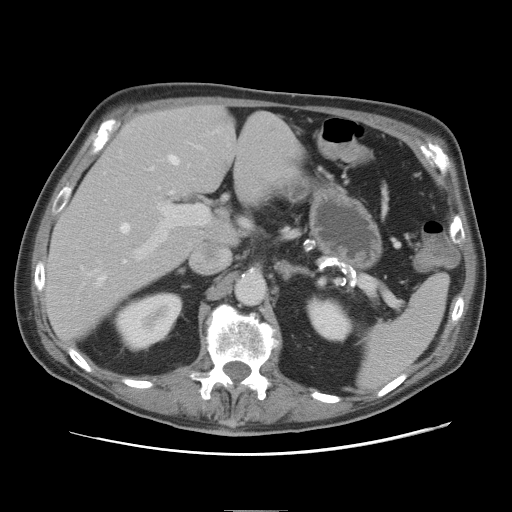
Contrast-enhanced abdominal CT, one axial slice; intravenous contrast given; soft-tissue window (W 400 / L 40 HU); 5 mm slice thickness; 512 × 512 image matrix, field of view 375 × 375 mm. Male patient, age 69 years. From the clinical record (not read from this slice): diagnosis: colorectal cancer liver metastases, imaged before liver resection; multiple liver metastases: no; largest metastasis: 8.5 cm; chemotherapy before resection: no.
Annotated regions visible in this slice (expert manual segmentation):
- hepatic veins: bounding box <98,154,180,284> (left, top, right, bottom; pixels)
- liver: <46,108,298,339>
- planned liver remnant (the part of the liver to remain after resection): <46,108,236,340>
- portal vein (with intrahepatic branches): <134,145,209,260>